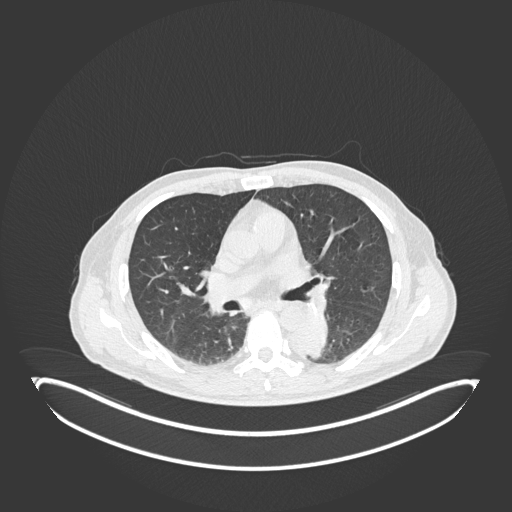
Chest CT, one axial slice. Slice 115 of 251 in the series (ordered by position). Reconstruction kernel B30f. Lung window (W 1500 / L -600 HU). 1 mm slice thickness. 512 × 512 image matrix, field of view 500 × 500 mm. Male patient, age 72 years. Case-level facts recorded for this patient, not image findings: clinical TNM (as recorded): T2b N0 M1.
Outlined on this slice (rectangle marked by the reading radiologist):
- lung tumour (recorded histology: adenocarcinoma): bounding box <290,313,330,363> (left, top, right, bottom; pixels)